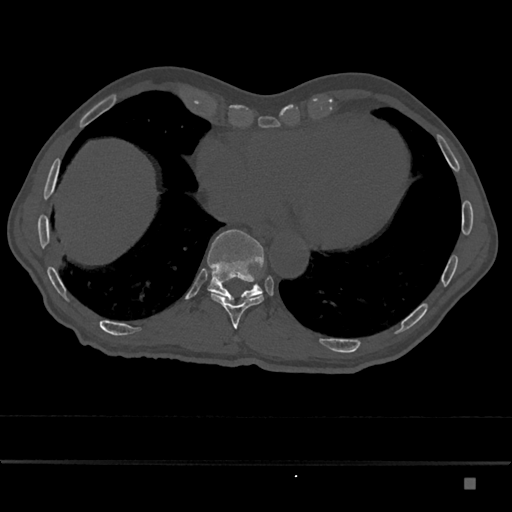
CT including the spine, one axial slice. Slice 719 of 797 in the series (ordered by position). Reconstruction kernel Br40s/3. 120 kVp. Bone window (W 1800 / L 400 HU). 512 × 512 image matrix. Patient: male, 72 years. From the clinical record (not read from this slice): primary cancer: prostate.
Outlined on this slice (semi-automatically segmented with operator editing):
- T10 vertebra: bounding box <211,293,264,329> (left, top, right, bottom; pixels)
- T11 vertebra: <207,230,264,302>